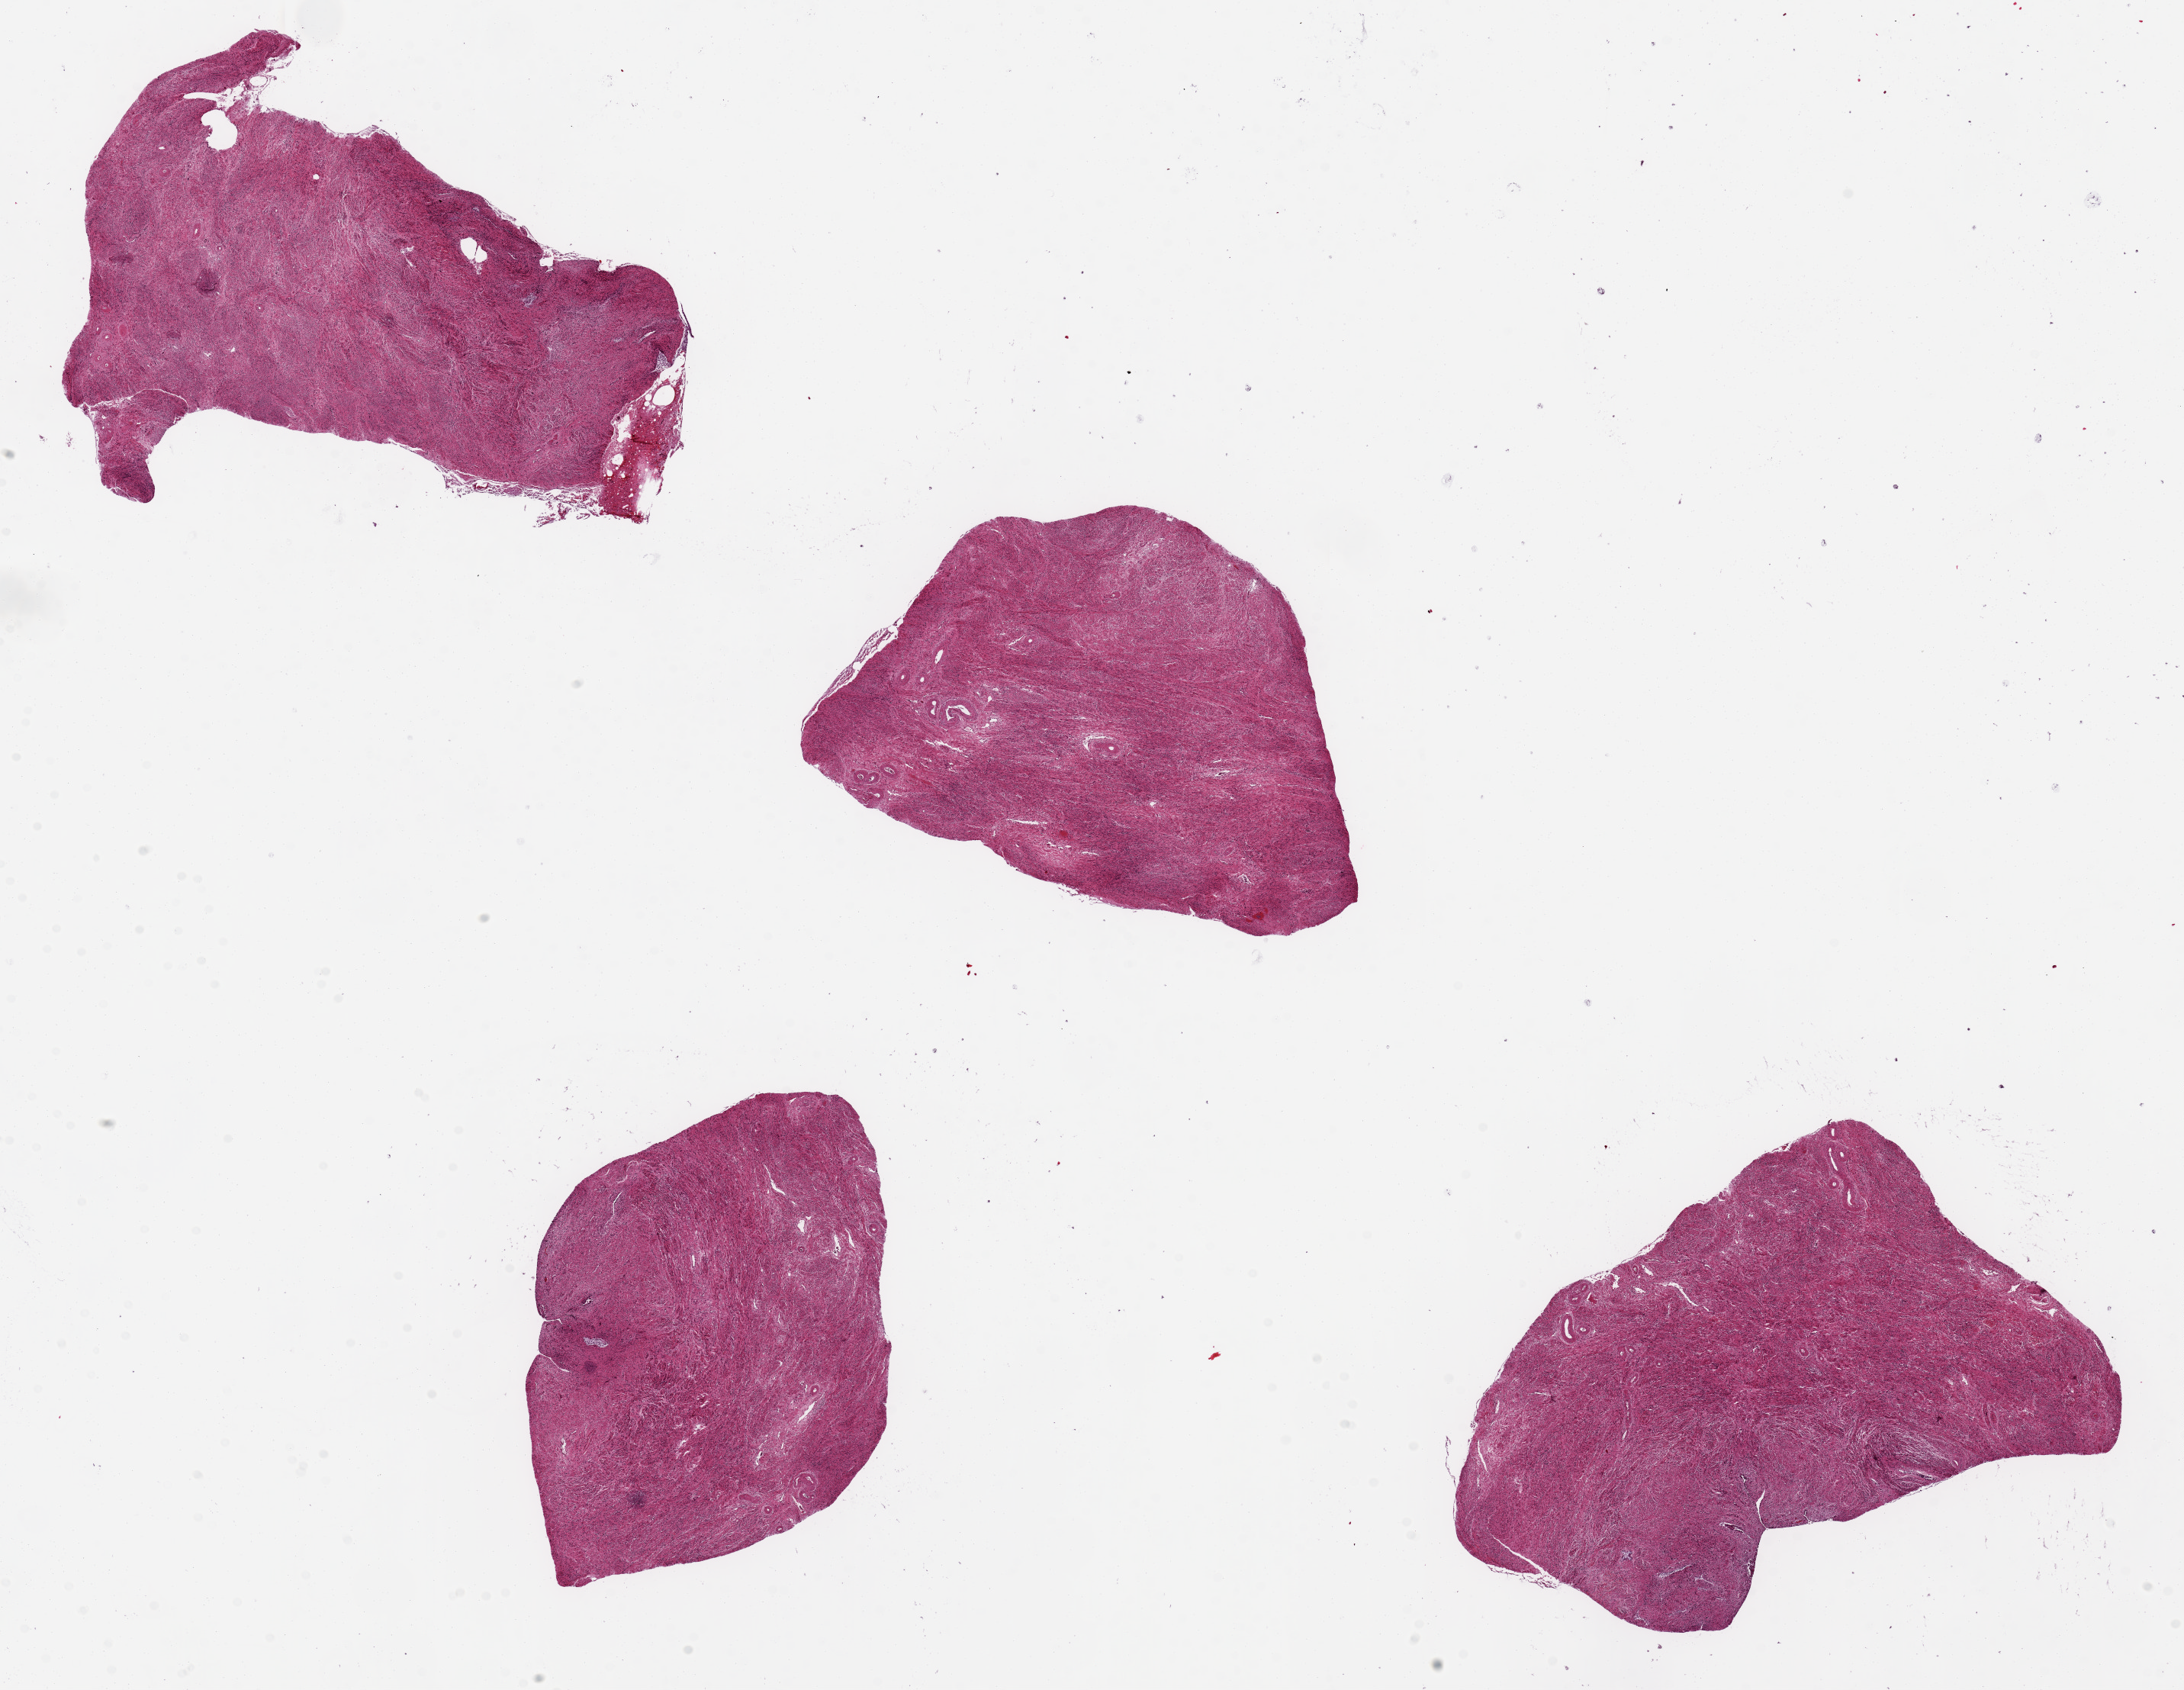
Digitized haematoxylin and eosin-stained section — low-resolution overview of the scanned area, about 22.6 x 17.5 mm (slide scanned at 20x), PAXgene-fixed, paraffin-embedded tissue, section of endocervix (target tissue), tissue donor sample. Female donor.
• reviewer comment on this tissue sample: 4 ~6x4mm aliquots. No visible/viable mucosa